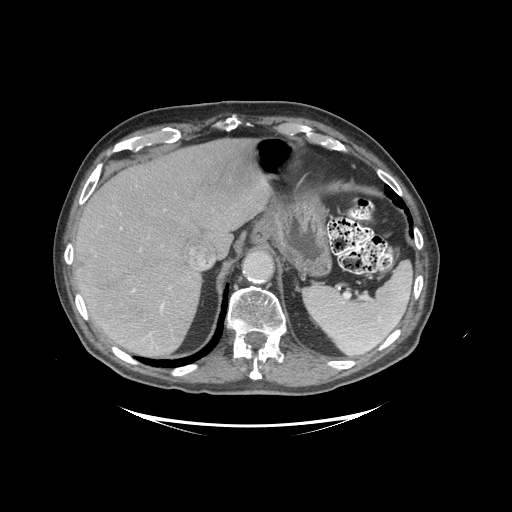
Contrast-enhanced abdominal CT (liver protocol), one axial slice; slice 75 of 99 in the series (ordered by position); soft-tissue window (W 400 / L 40 HU); 512 × 512 image matrix, field of view 460 × 460 mm. From the clinical record (not read from this slice): diagnosis: hepatocellular carcinoma (patient treated with transarterial chemoembolisation; whether this scan precedes or follows treatment is not stated here); TNM stage (as recorded): Stage-I; Child-Pugh class: A; tumour differentiation: moderately differentiated; tumour nodularity: uninodular.
Annotated regions visible in this slice (semi-automatically segmented with operator editing):
- liver parenchyma outside the tumour (the mass and vessels are separate outlines, so this box may not span the whole liver): box from (x=74, y=138) to (x=270, y=356) px
- liver vessels: (x=132, y=263)–(x=204, y=337)